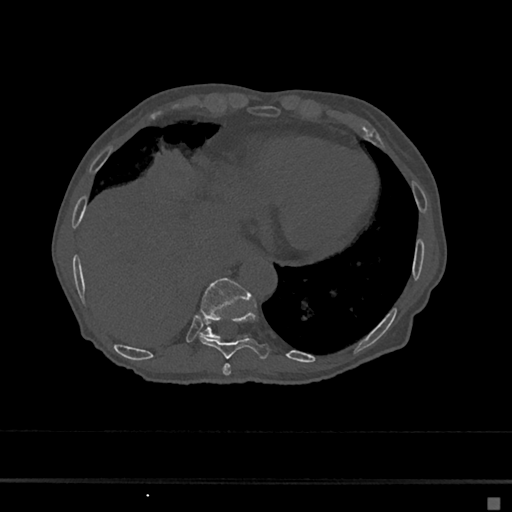
CT including the spine, one axial slice; position 259 of 797 along the scan axis; reconstruction kernel Br40s/3; bone window (W 1800 / L 400 HU); 0.5 mm slice thickness; 512 × 512 image matrix, field of view 360 × 360 mm. Female patient, age 68 years. From the clinical record (not read from this slice): primary cancer: renal.
Outlined on this slice (semi-automatic segmentation, software-assisted and operator-edited):
- T10 vertebra: bounding box <200,278,250,339> (left, top, right, bottom; pixels)
- T8 vertebra: <222,364,231,376>
- T9 vertebra: <199,310,271,360>